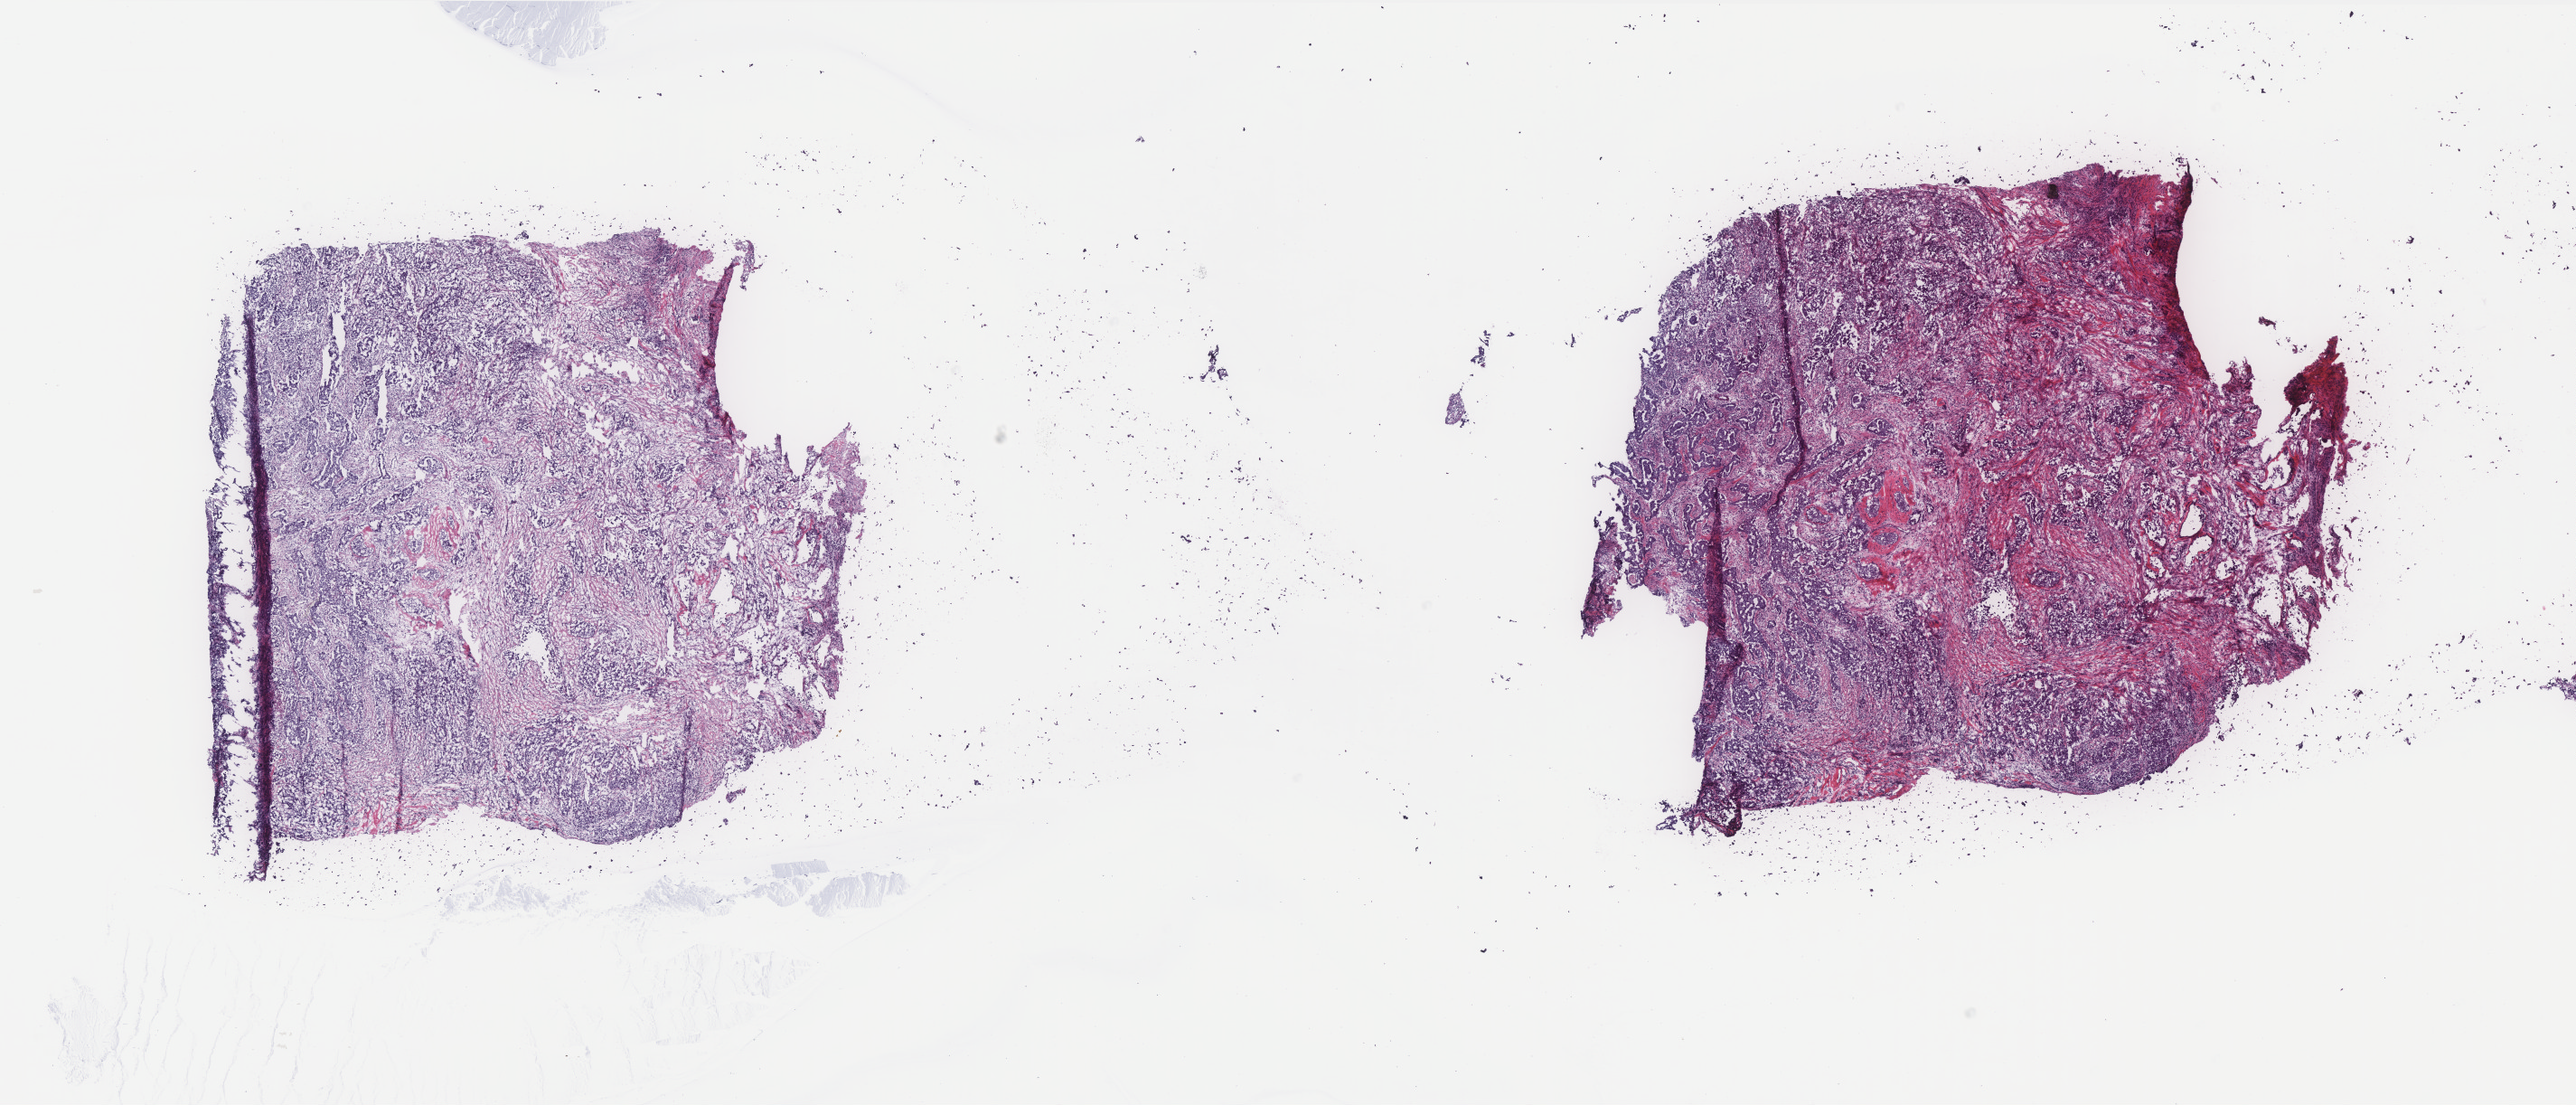
H&E-stained whole-slide image — a low-resolution overview of the entire scanned area, about 22.8 x 9.8 mm (from a 40x scan). Frozen section from the bottom of the tissue portion. Breast, primary tumour sample. Female, age 43 years at initial diagnosis. Composition of this section per pathologist review: tumour cells 80%, tumour nuclei 85%, normal cells 0%, stromal cells 19%, necrosis 1%. Inflammatory infiltration, as recorded: lymphocyte infiltration 4%, monocyte infiltration 0%, neutrophil infiltration 0%.
Laterality: left. AJCC pathologic stage: IIA (6th edition). Lymph nodes positive (case pathology): 1 of 16 examined. TNM: T1c N1a M0. Pathologic diagnosis: Infiltrating duct carcinoma, NOS.